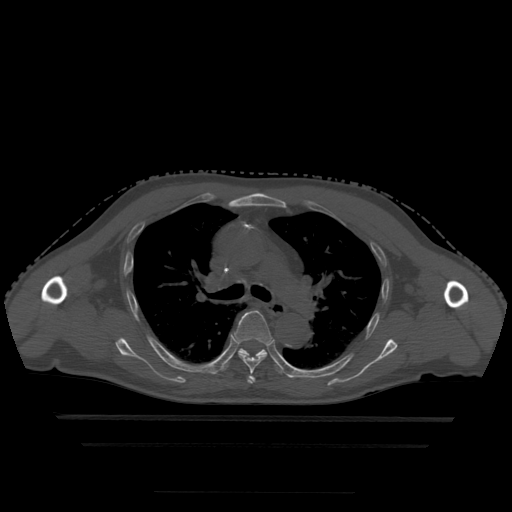
CT including the spine, one axial slice. Position 331 of 522 along the scan axis. Bone window (W 1800 / L 400 HU). 1.25 mm slice thickness. 512 × 512 image matrix. Patient age 68 years. From the clinical record (not read from this slice): primary cancer: urothelial.
Structures marked on this image (semi-automatic segmentation, software-assisted and operator-edited):
- T4 vertebra: bounding box (x1, y1, x2, y2) in pixels: (248, 376, 255, 384)
- T5 vertebra: (234, 311, 273, 382)
- T6 vertebra: (224, 348, 283, 375)